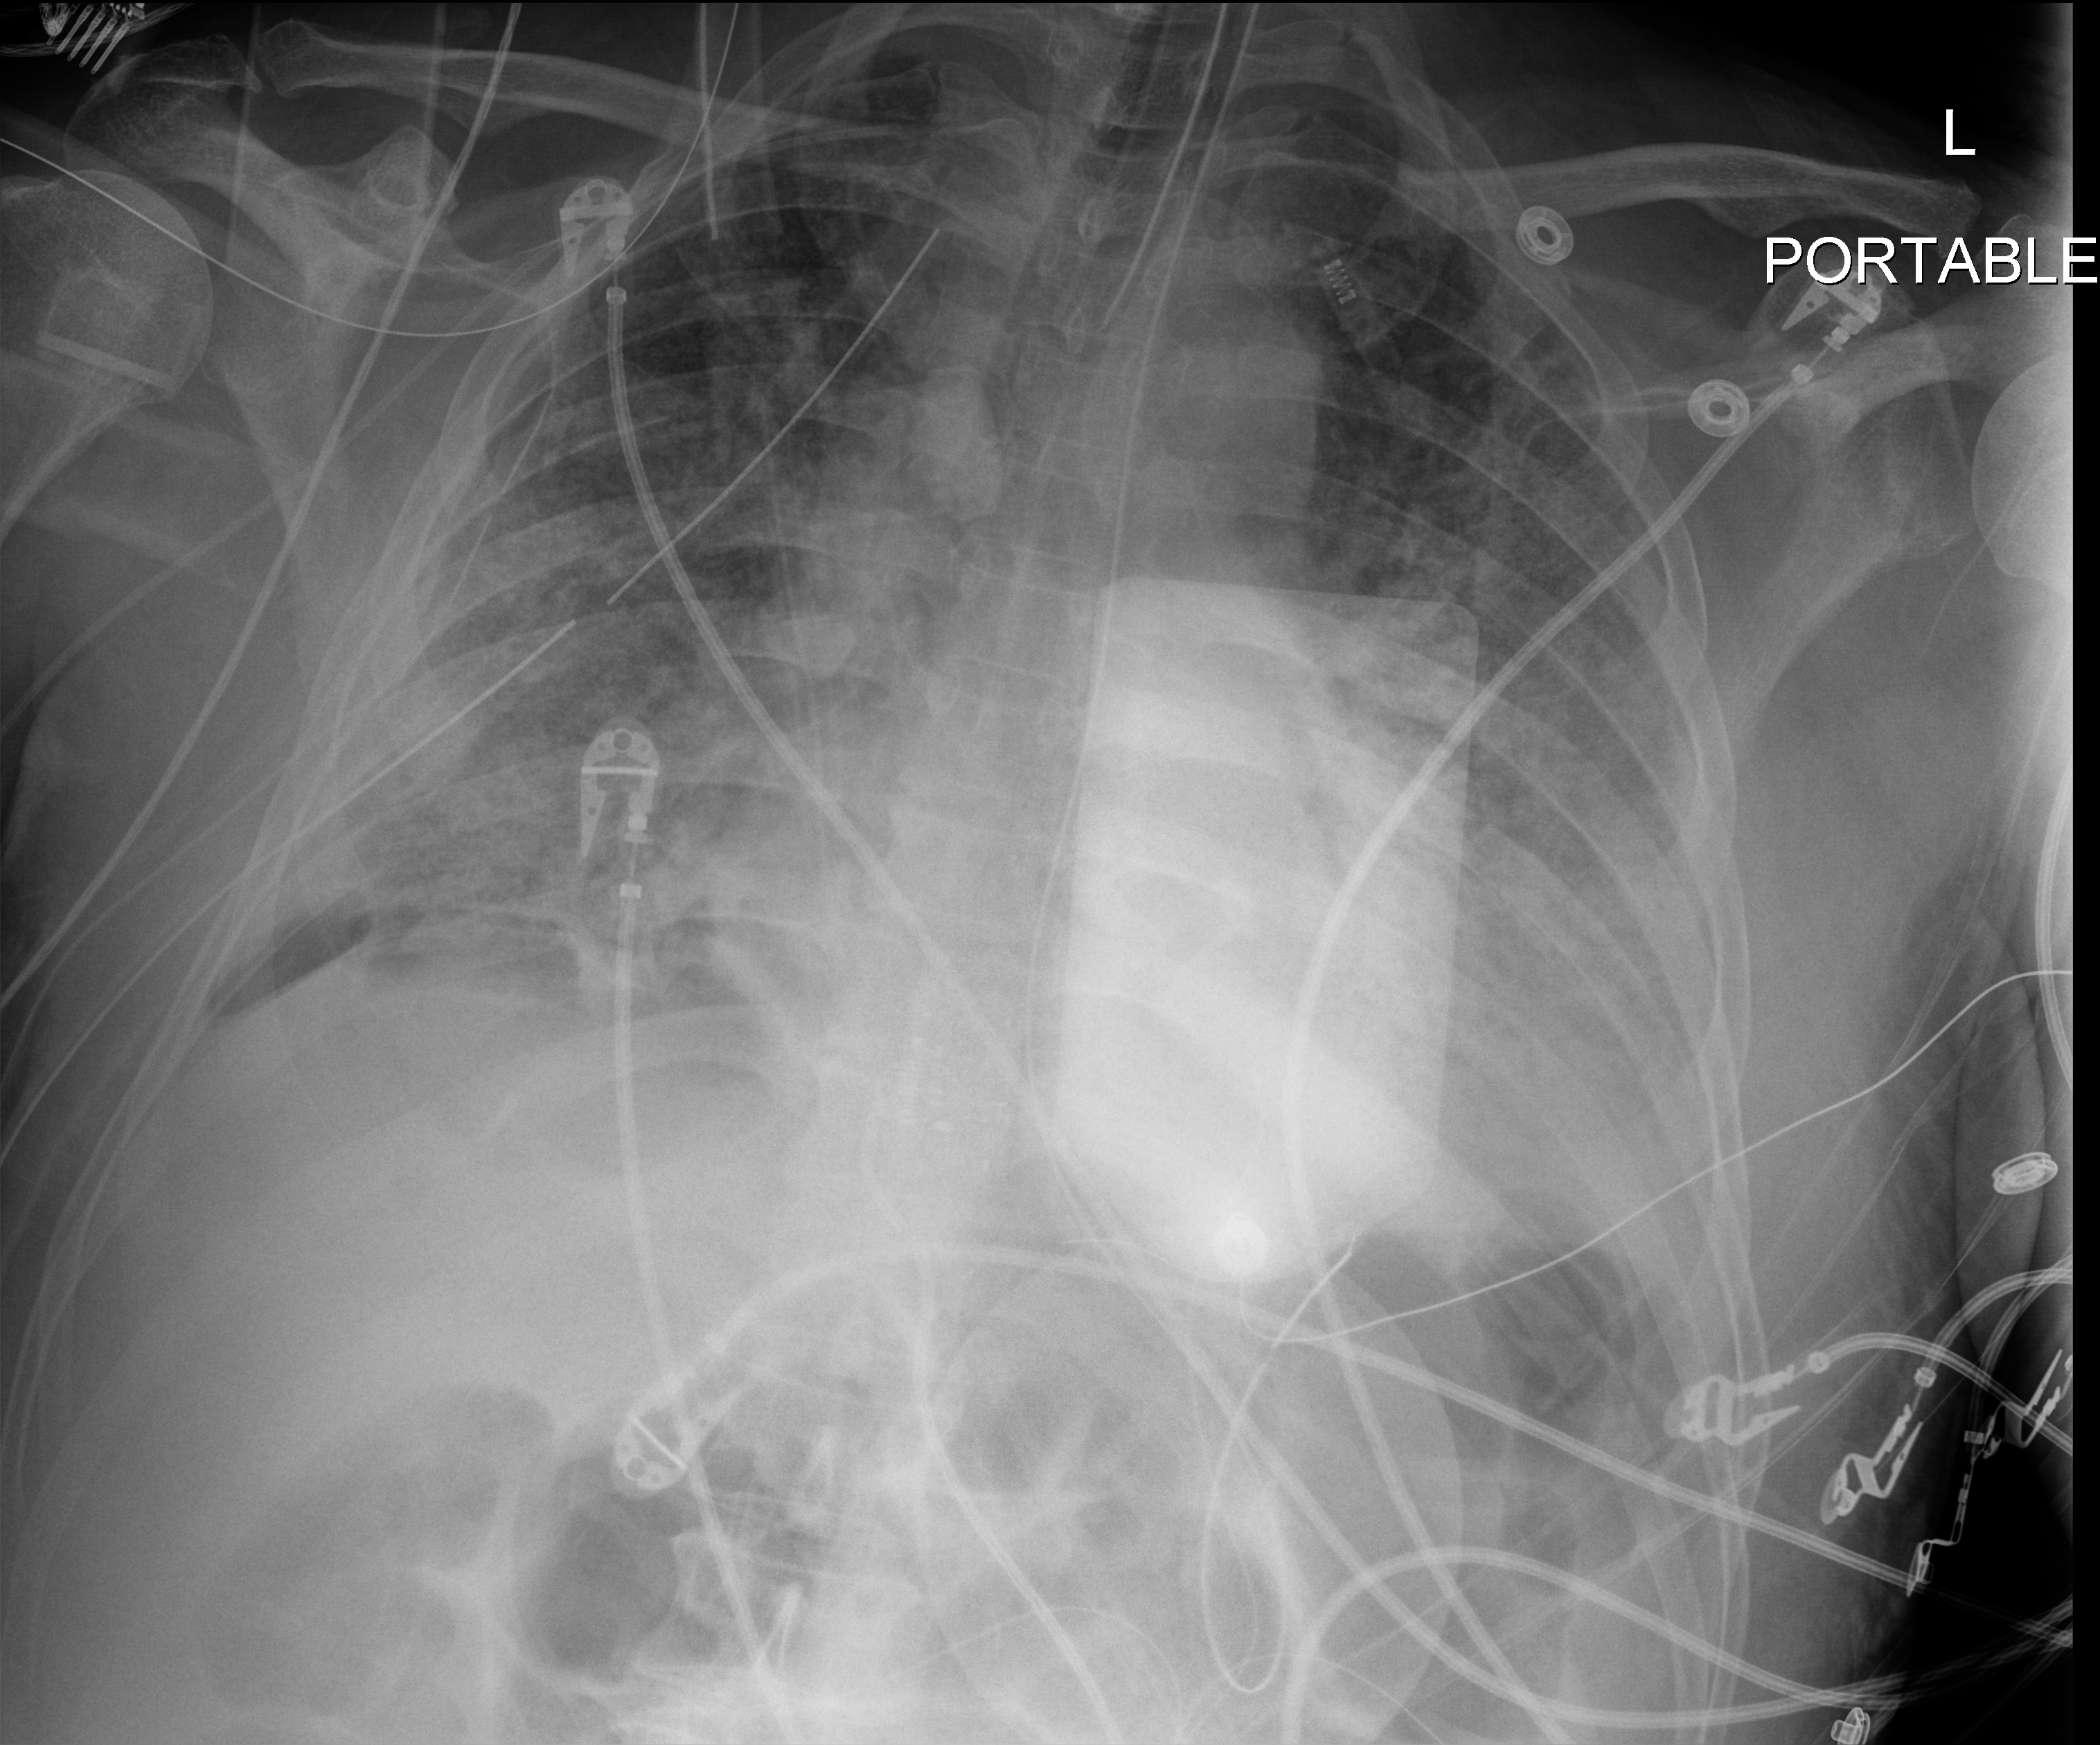
Chest radiograph. Male patient hospitalised with COVID-19, age 60–74 years.
From the hospital-stay record, not from the radiograph (when in the stay this image was taken is not recorded): length of hospital stay: 37 days.